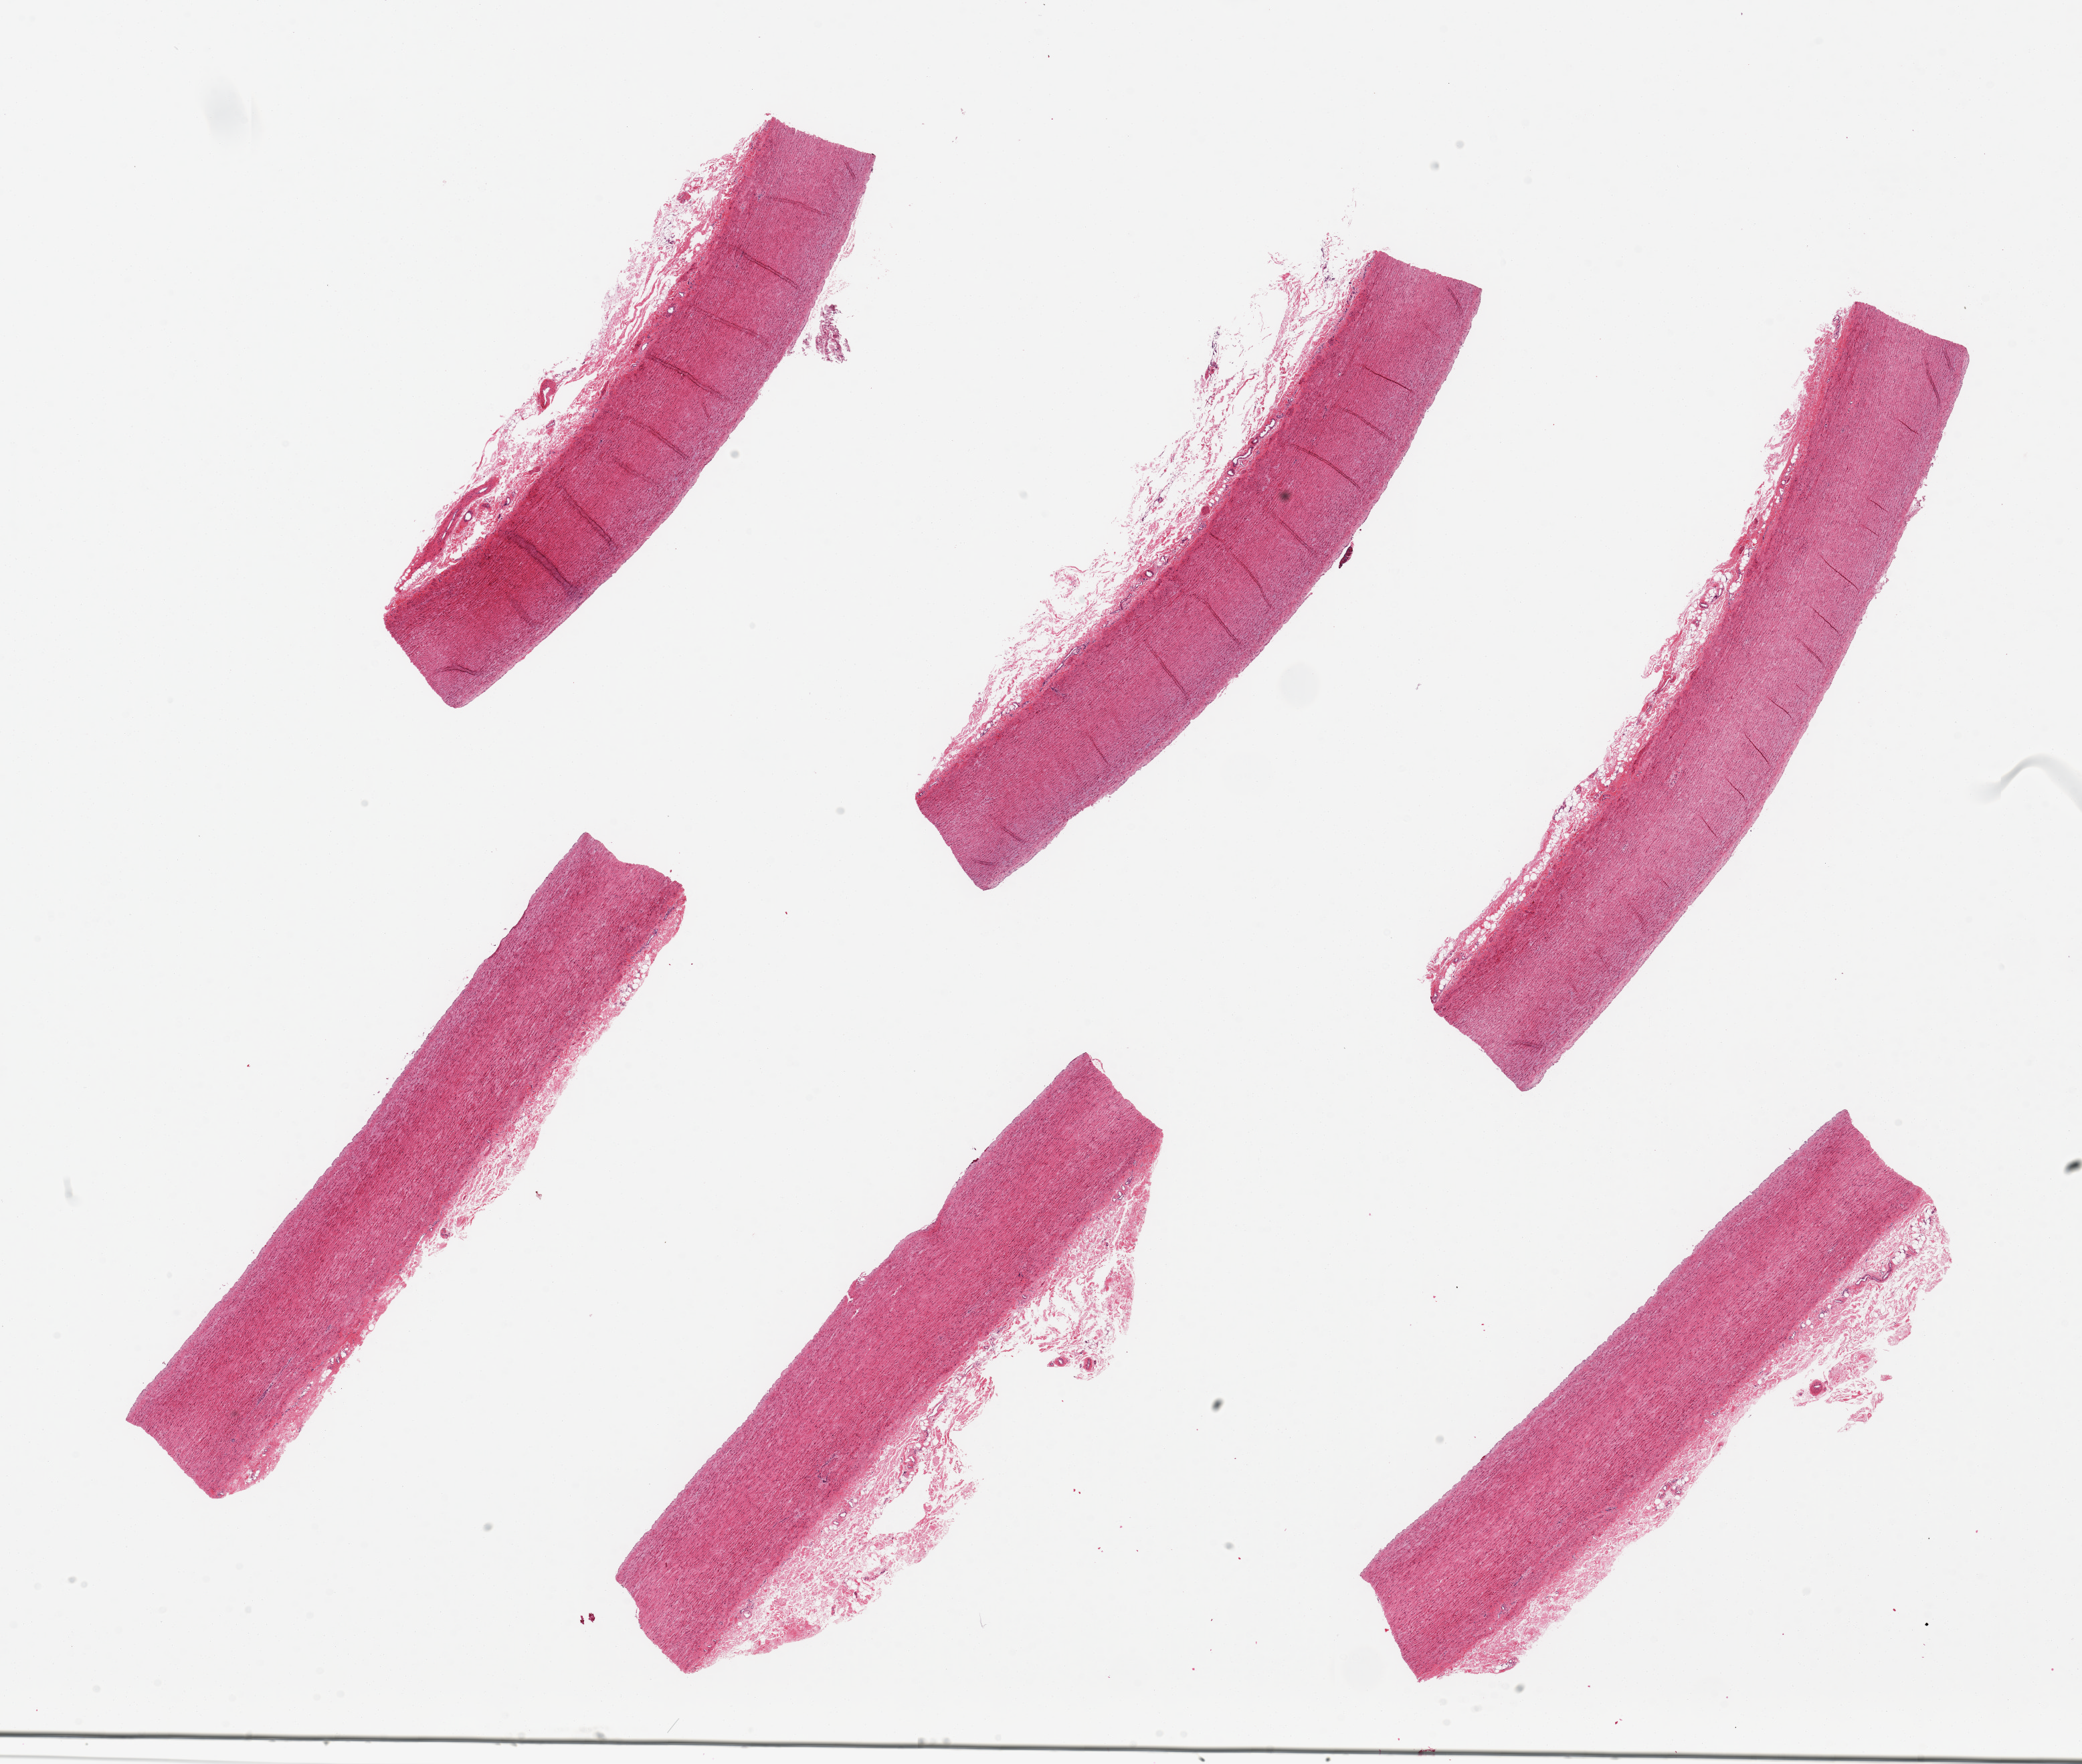
Whole-slide image, H&E stain, brightfield, whole scanned area (about 24.6 x 20.9 mm, acquisition: 20x scan) shown as a low-resolution overview; PAXgene-fixed paraffin-embedded (PFPE) section; sampled site (target tissue): aorta; tissue donor sample. Donor: male.
• review note (as recorded): 6 pieces ~9x2mm. Minimal atherosis, several with adherent layer of serosal fat up to ~0.5m